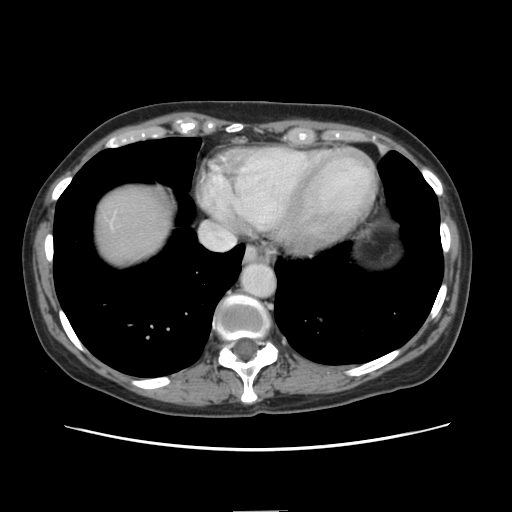
Contrast-enhanced abdominal CT, one axial slice; position 131 of 141 along the scan axis; 120 kVp; intravenous contrast given; soft-tissue window (W 400 / L 40 HU); 2.5 mm slice thickness; 512 × 512 image matrix, field of view 350 × 350 mm. Female patient, age 63 years. Case-level facts recorded for this patient, not image findings: diagnosis: colorectal cancer liver metastases, imaged before liver resection; multiple liver metastases: yes; largest metastasis: 3.2 cm.
Structures marked on this image (outlined manually by an expert reader):
- liver: bounding box [x1, y1, x2, y2] px = [95, 184, 171, 268]